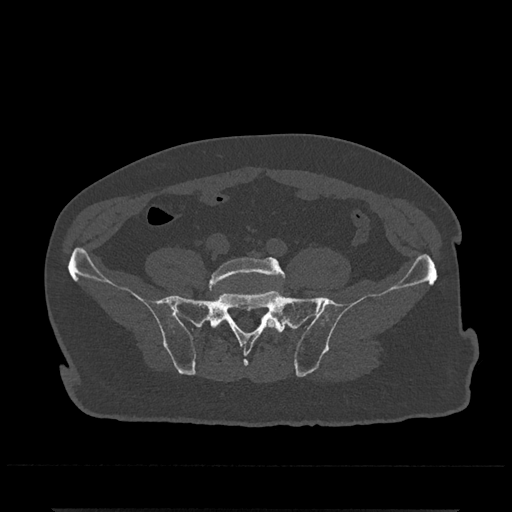
CT including the spine, one axial slice. Position 45 of 797 along the scan axis. Reconstruction kernel Br40s/3. 120 kVp. Bone window (W 1800 / L 400 HU). 0.5 mm slice thickness. 512 × 512 image matrix. Patient: male, 67 years. From the clinical record (not read from this slice): primary cancer: prostate.
Outlined on this slice (semi-automatically segmented with operator editing):
- L5 vertebra: bounding box (x1, y1, x2, y2) in pixels: (209, 257, 285, 329)